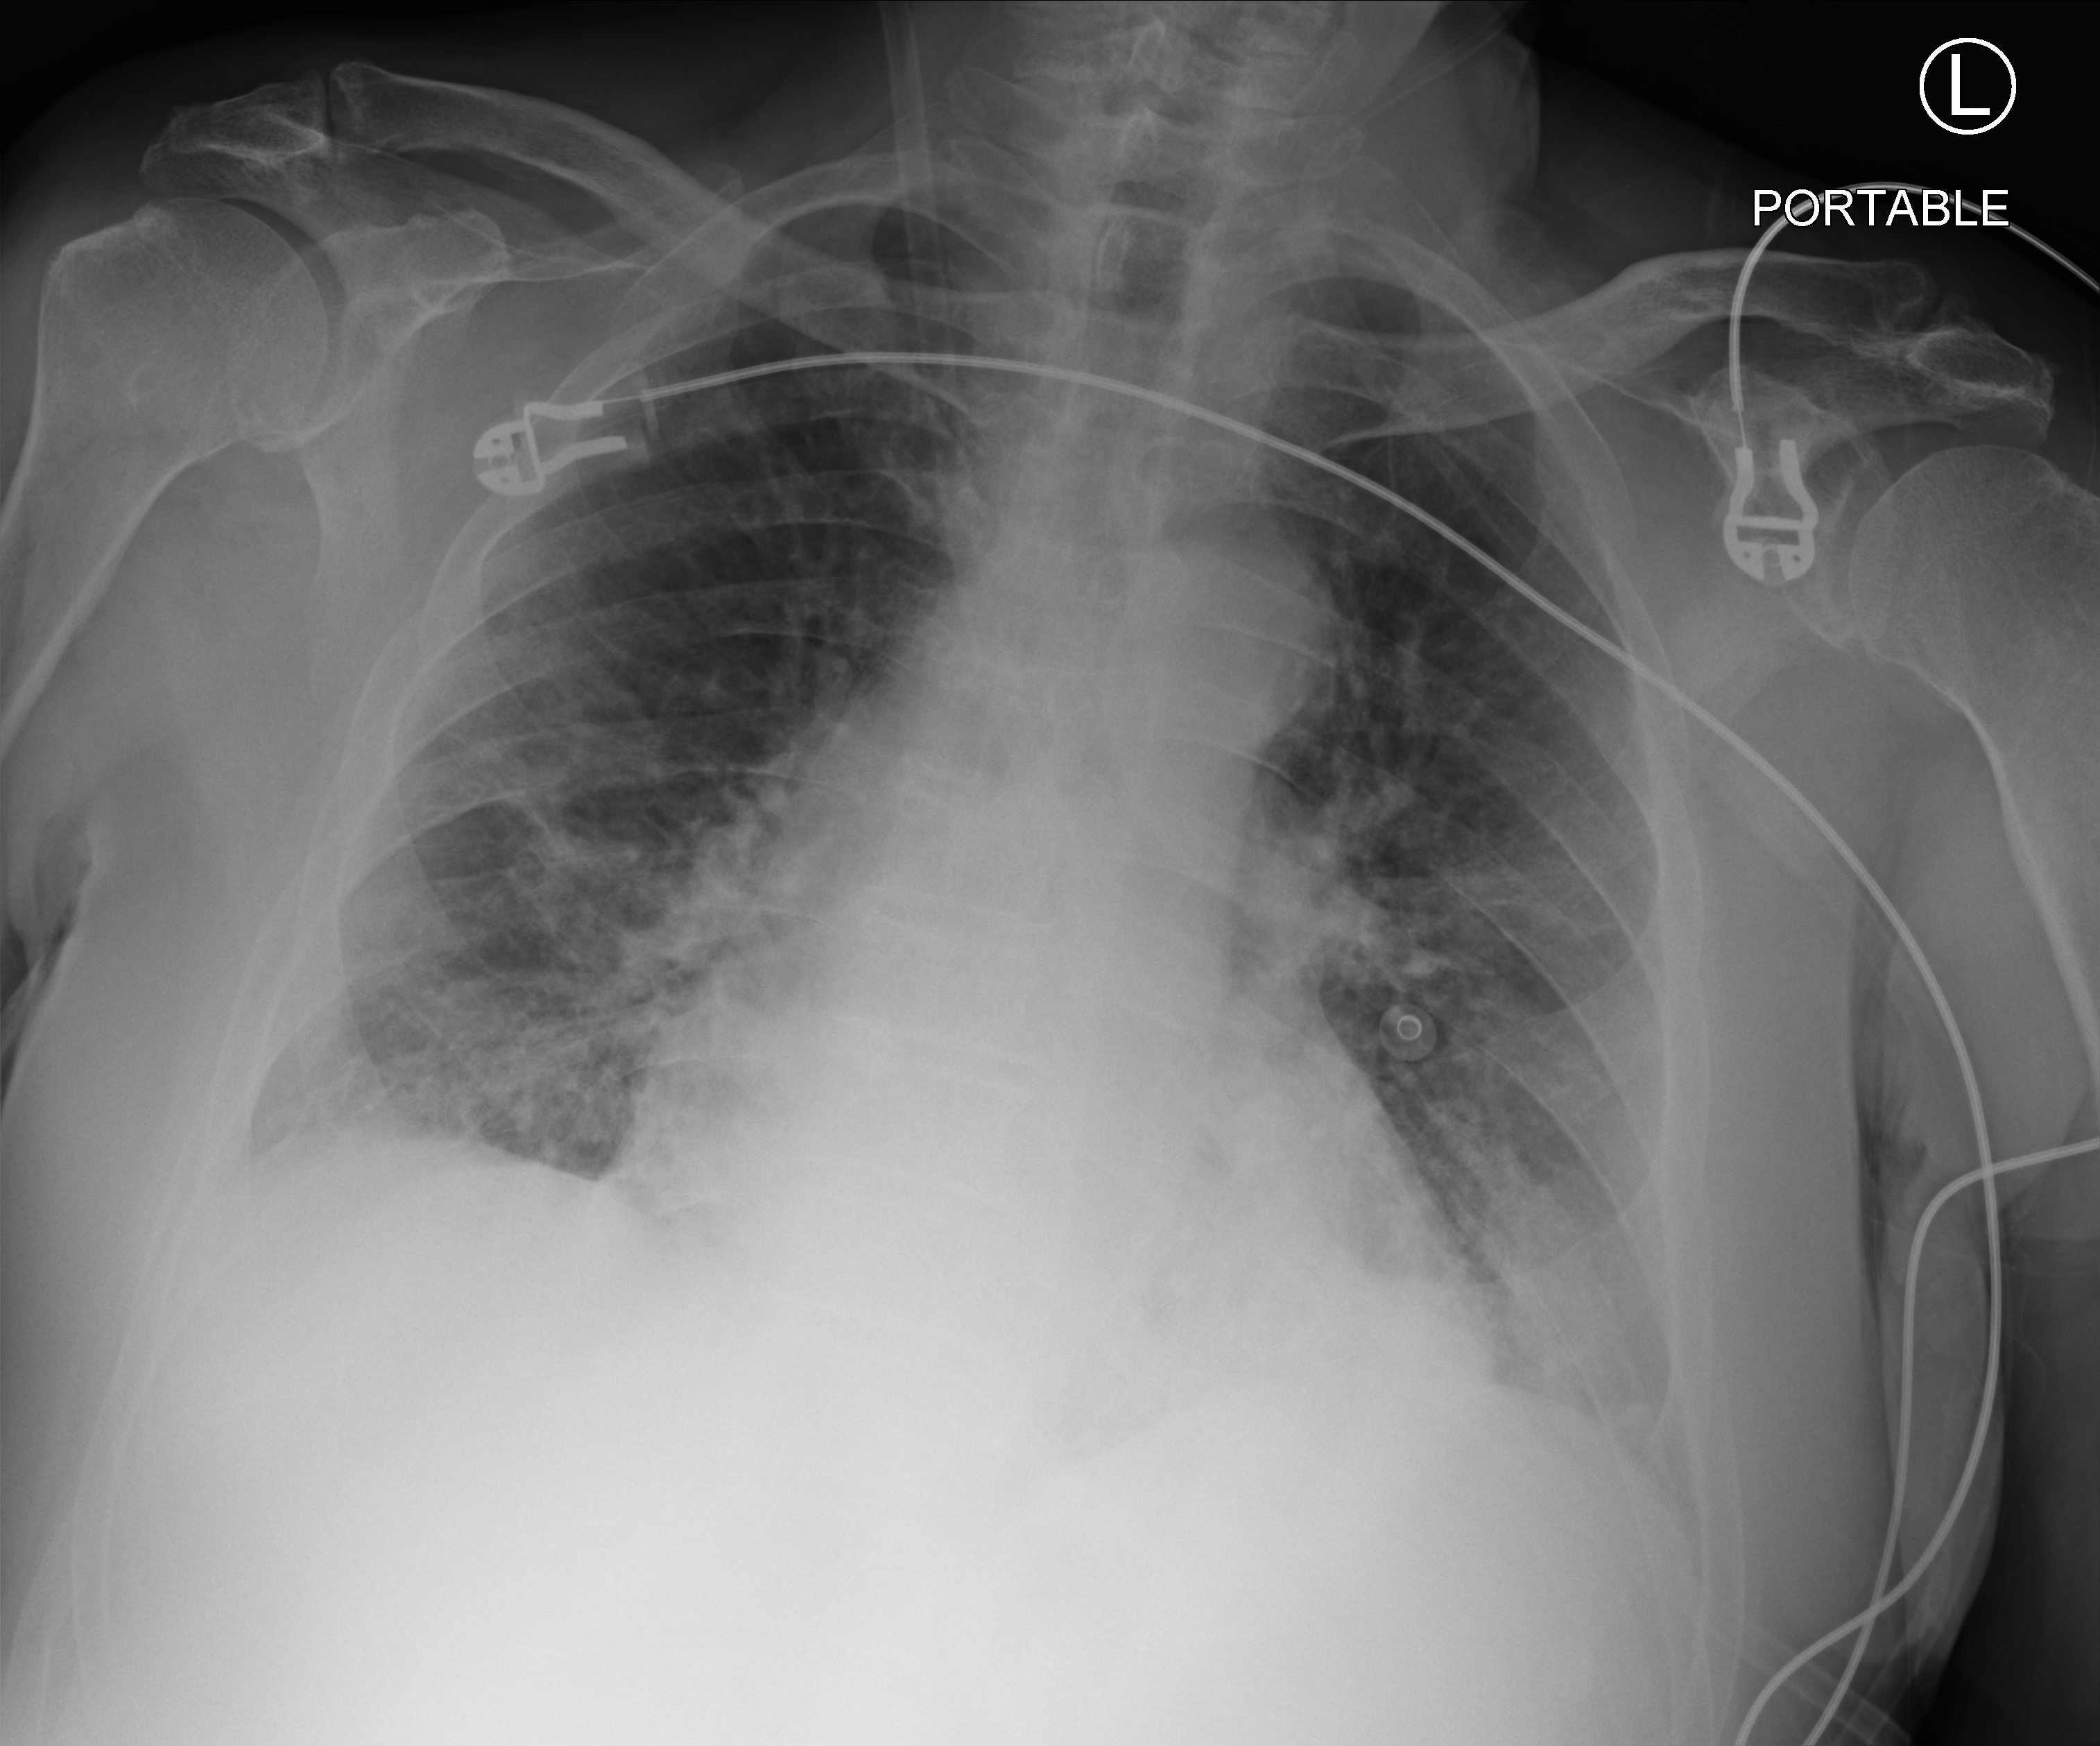
Bedside chest radiograph (computed radiography); anteroposterior (AP) projection. Male patient hospitalised with COVID-19, age 75–90 years.
From the hospital-stay record, not from the radiograph (when in the stay this image was taken is not recorded):
- mechanically ventilated during this hospital stay: no